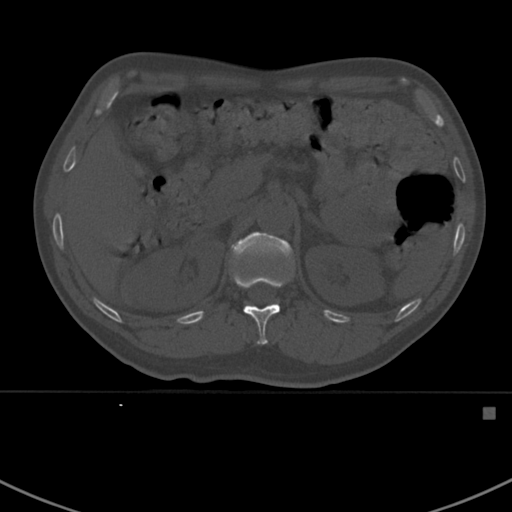
CT including the spine, one axial slice; slice 323 of 412 in the series (ordered by position); reconstruction kernel Br40s; 120 kVp; bone window (W 1800 / L 400 HU); 1.5 mm slice thickness; 512 × 512 image matrix, field of view 358 × 358 mm. Patient: male, 59 years. Case-level facts recorded for this patient, not image findings: primary cancer: prostate.
Annotated regions visible in this slice (semi-automatic segmentation, software-assisted and operator-edited):
- L1 vertebra: bounding box <231,232,293,262> (left, top, right, bottom; pixels)
- T12 vertebra: <233,275,287,345>